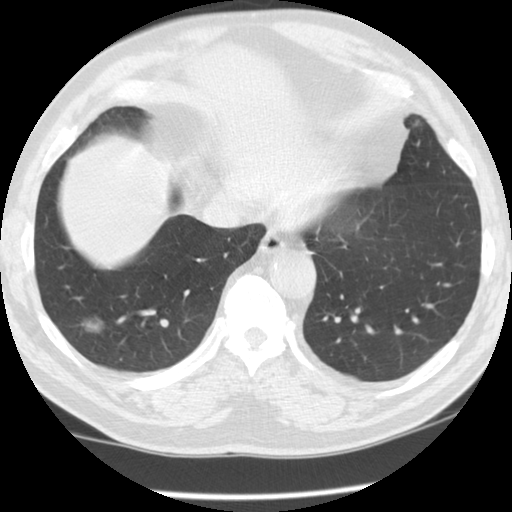
Chest CT (low-dose screening protocol), one axial image. Second annual screen. Lung window (W 1500 / L -600 HU). Standard (soft-tissue) reconstruction kernel (STANDARD). Slice 87 of 115 in the series. Male participant, aged 62 years at enrolment.
- Expert-annotated lung lesion, box from (x=65, y=304) to (x=127, y=355) px.
- Screening reader's record for this exam (one nodule recorded; not confirmed to be the boxed lesion): non-calcified nodule or mass ≥4 mm, right lower lobe, 13 × 11 mm, smooth margins, ground glass attenuation, pre-existing on the prior screen: yes; interval growth: no.
- Official screen result: positive, no significant change: stable abnormalities potentially related to lung cancer, unchanged since the prior screening exam.